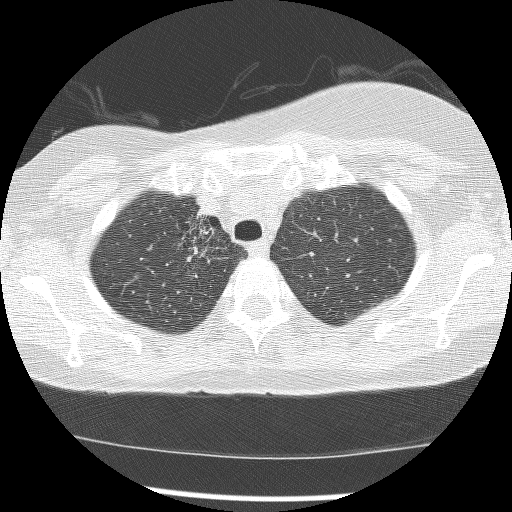
Axial slice from a low-dose chest CT screening exam; first (baseline) screen; lung window (W 1500 / L -600 HU); slice 31 of 172 in the series. Female, age 56 years at enrolment. Current smoker at enrolment.
Lesion marked by an expert reader, bounding box <166,211,225,279> (left, top, right, bottom; pixels). The screening reader recorded 2 non-calcified nodules or masses ≥4 mm on this exam; which of them this box marks is not recorded.